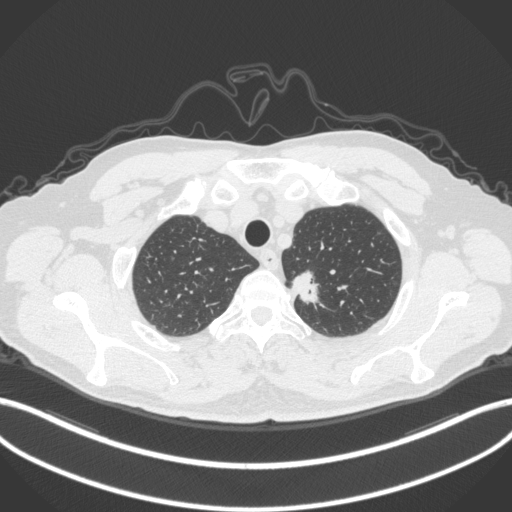
Chest CT, one axial slice; slice 325 of 382 in the series (ordered by position); reconstruction kernel B31f; 120 kVp; lung window (W 1500 / L -600 HU); 1 mm slice thickness; 512 × 512 image matrix, field of view 400 × 400 mm. Patient: male, 64 years. From the clinical record (not read from this slice): clinical TNM (as recorded): T1c N0 M0.
Structures marked on this image (rectangle marked by the reading radiologist):
- lung tumour (recorded histology: adenocarcinoma): bounding box <291,265,324,309> (left, top, right, bottom; pixels)